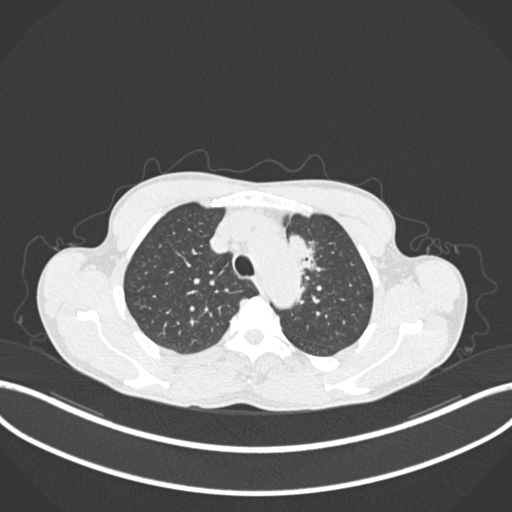
Chest CT, one axial slice. Position 158 of 211 along the scan axis. Reconstruction kernel B30f. 120 kVp. Lung window (W 1500 / L -600 HU). 512 × 512 image matrix, field of view 400 × 400 mm. Patient: male, 58 years. From the clinical record (not read from this slice): clinical TNM (as recorded): T1c N1 M0.
Structures marked on this image (rectangle marked by the reading radiologist):
- lung tumour (recorded histology: adenocarcinoma): bounding box [x1, y1, x2, y2] px = [281, 223, 327, 274]